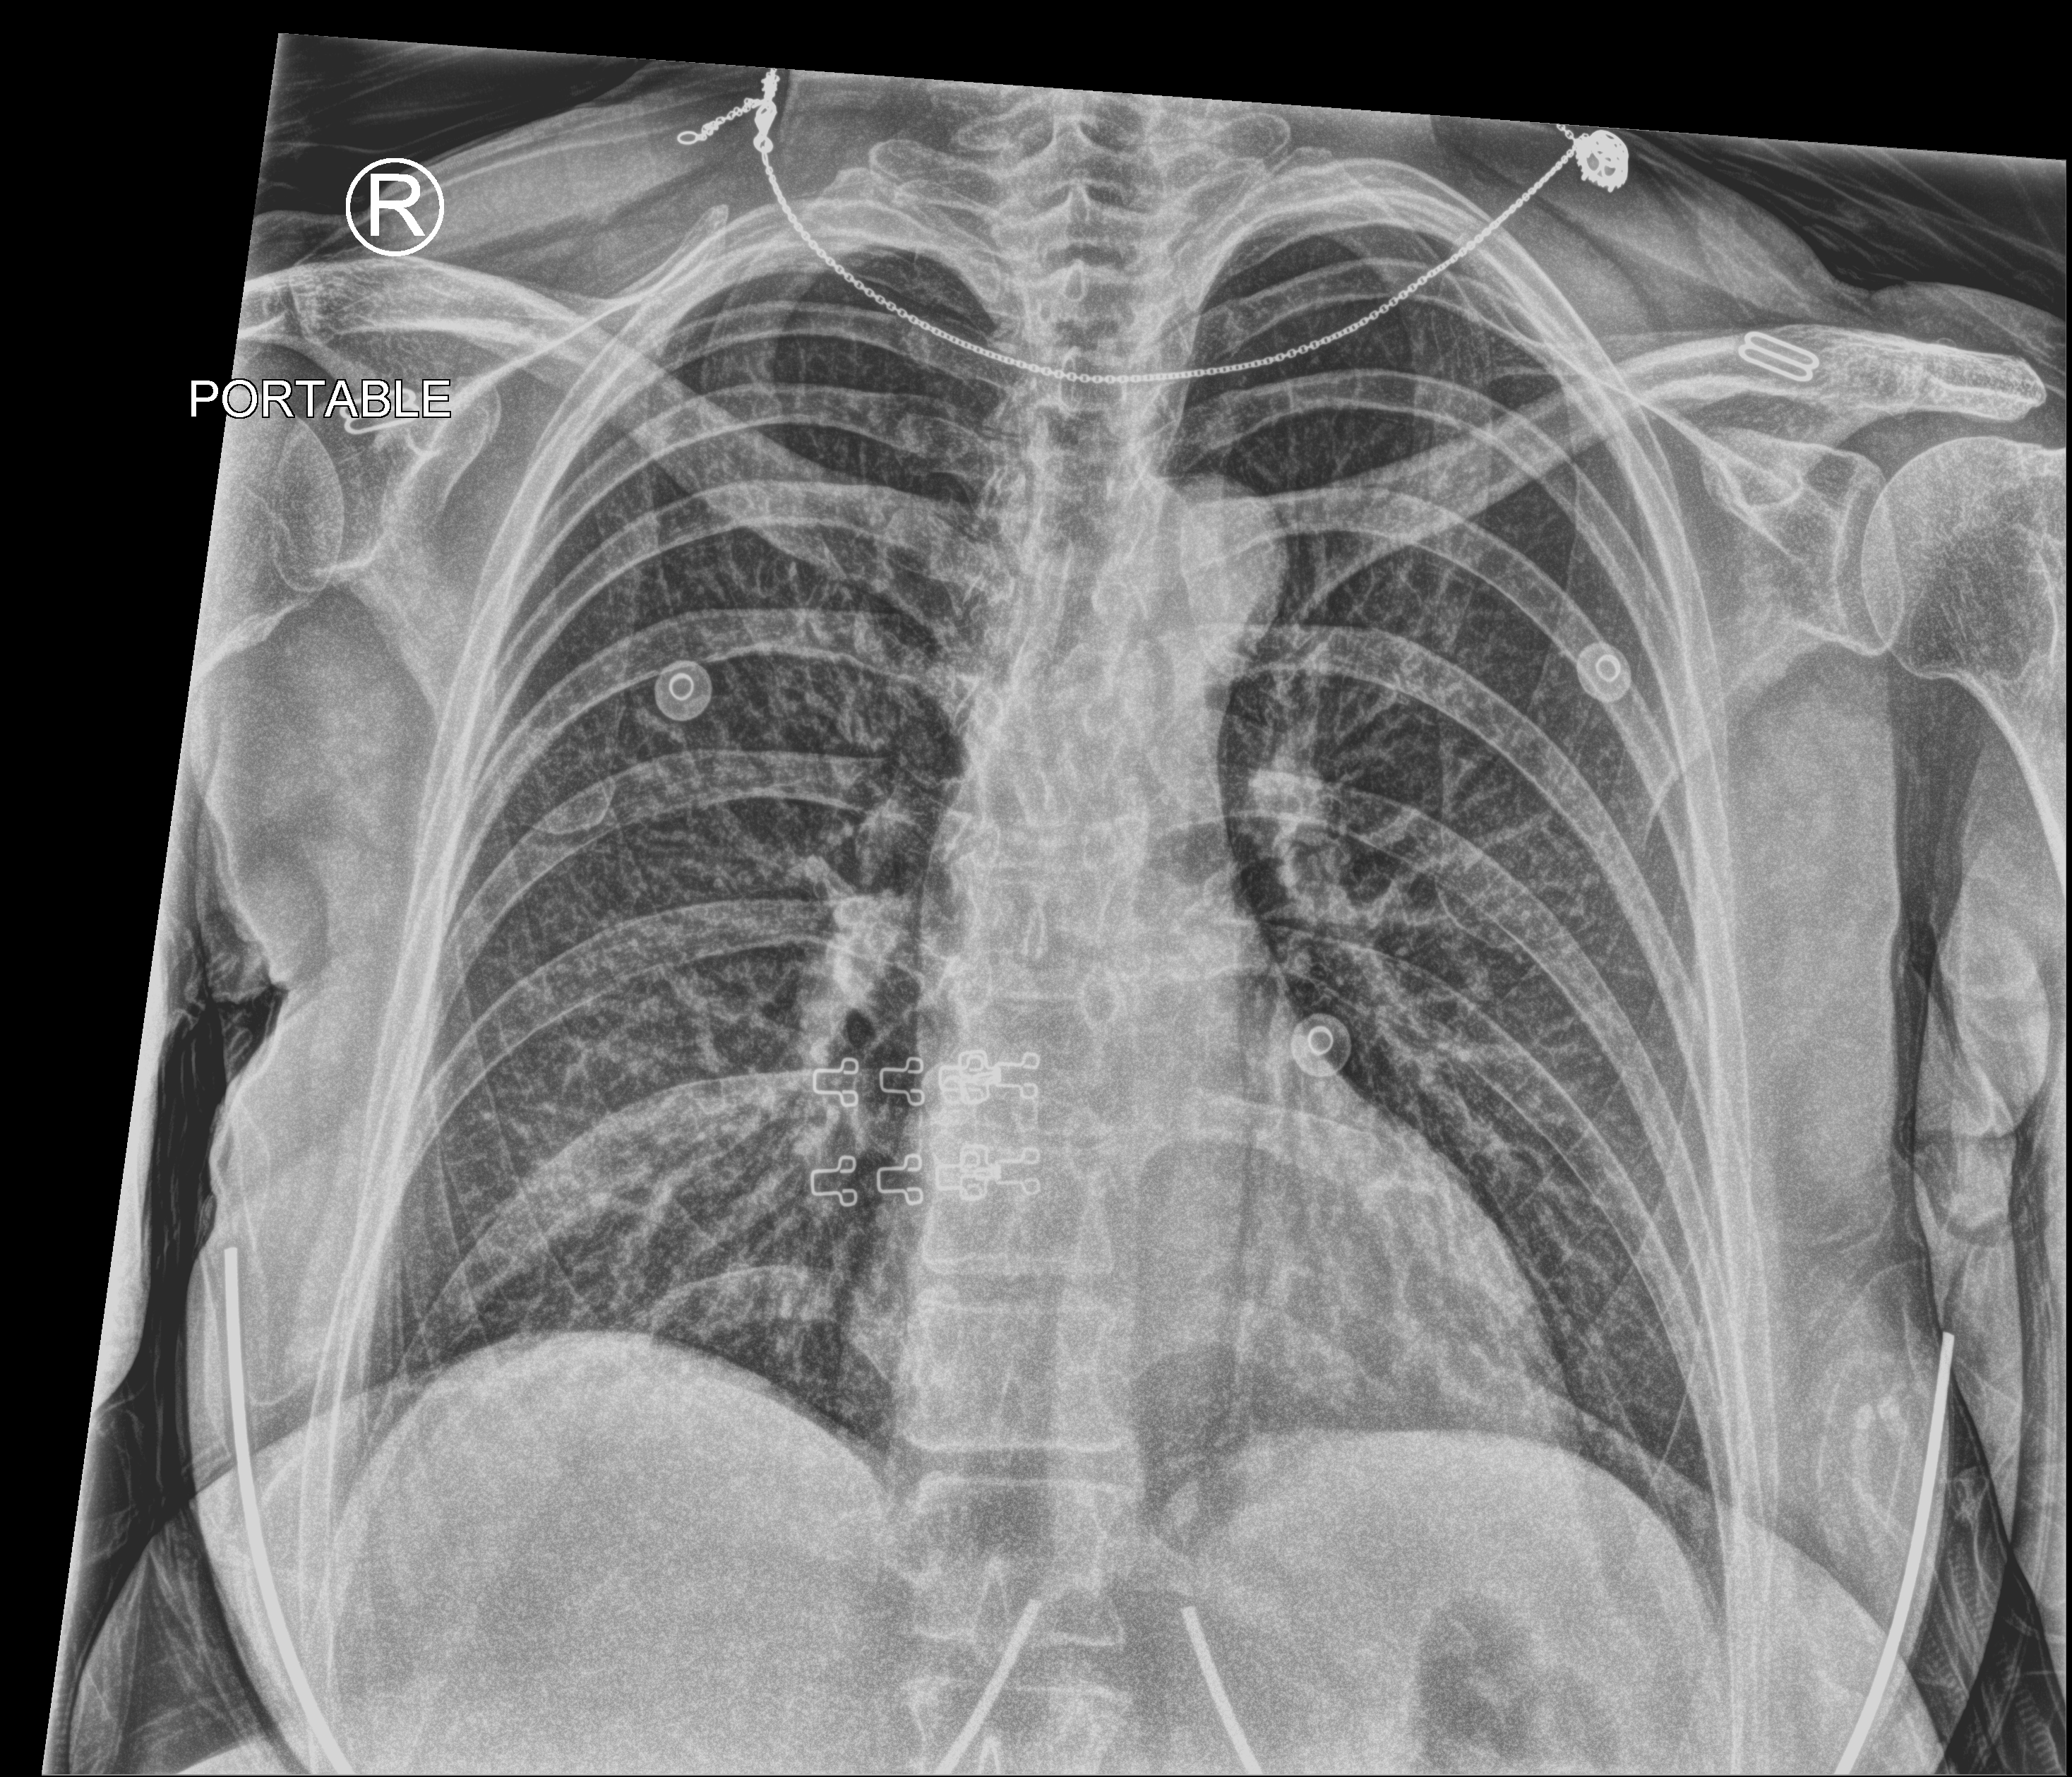
Portable chest radiograph; anteroposterior (AP) projection. Female patient hospitalised with COVID-19, age 18–59 years.
From the hospital-stay record, not from the radiograph (when in the stay this image was taken is not recorded): mechanically ventilated during this hospital stay: no; length of hospital stay: 1 day; admitted to intensive care during this hospital stay: no.